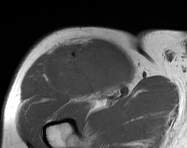
MRI of an extremity soft-tissue mass, one axial slice. Slice 103 of 114 in the series (ordered by position). MR volume resampled by the dataset authors to the PET/CT grid (not the native acquisition matrix). 3.27 mm slice thickness. 187 × 148 image matrix. Male patient. Case-level facts recorded for this patient, not image findings: histological type: pleiomorphic leiomyosarcoma; grade: intermediate; site of the primary tumour: right thigh.
Outlined on this slice (expert contour drawn on MRI and transferred to this co-registered scan by the dataset authors):
- gross tumour volume including surrounding oedema: bounding box <59,40,128,99> (left, top, right, bottom; pixels)
- gross tumour volume (mass): <61,45,128,98>